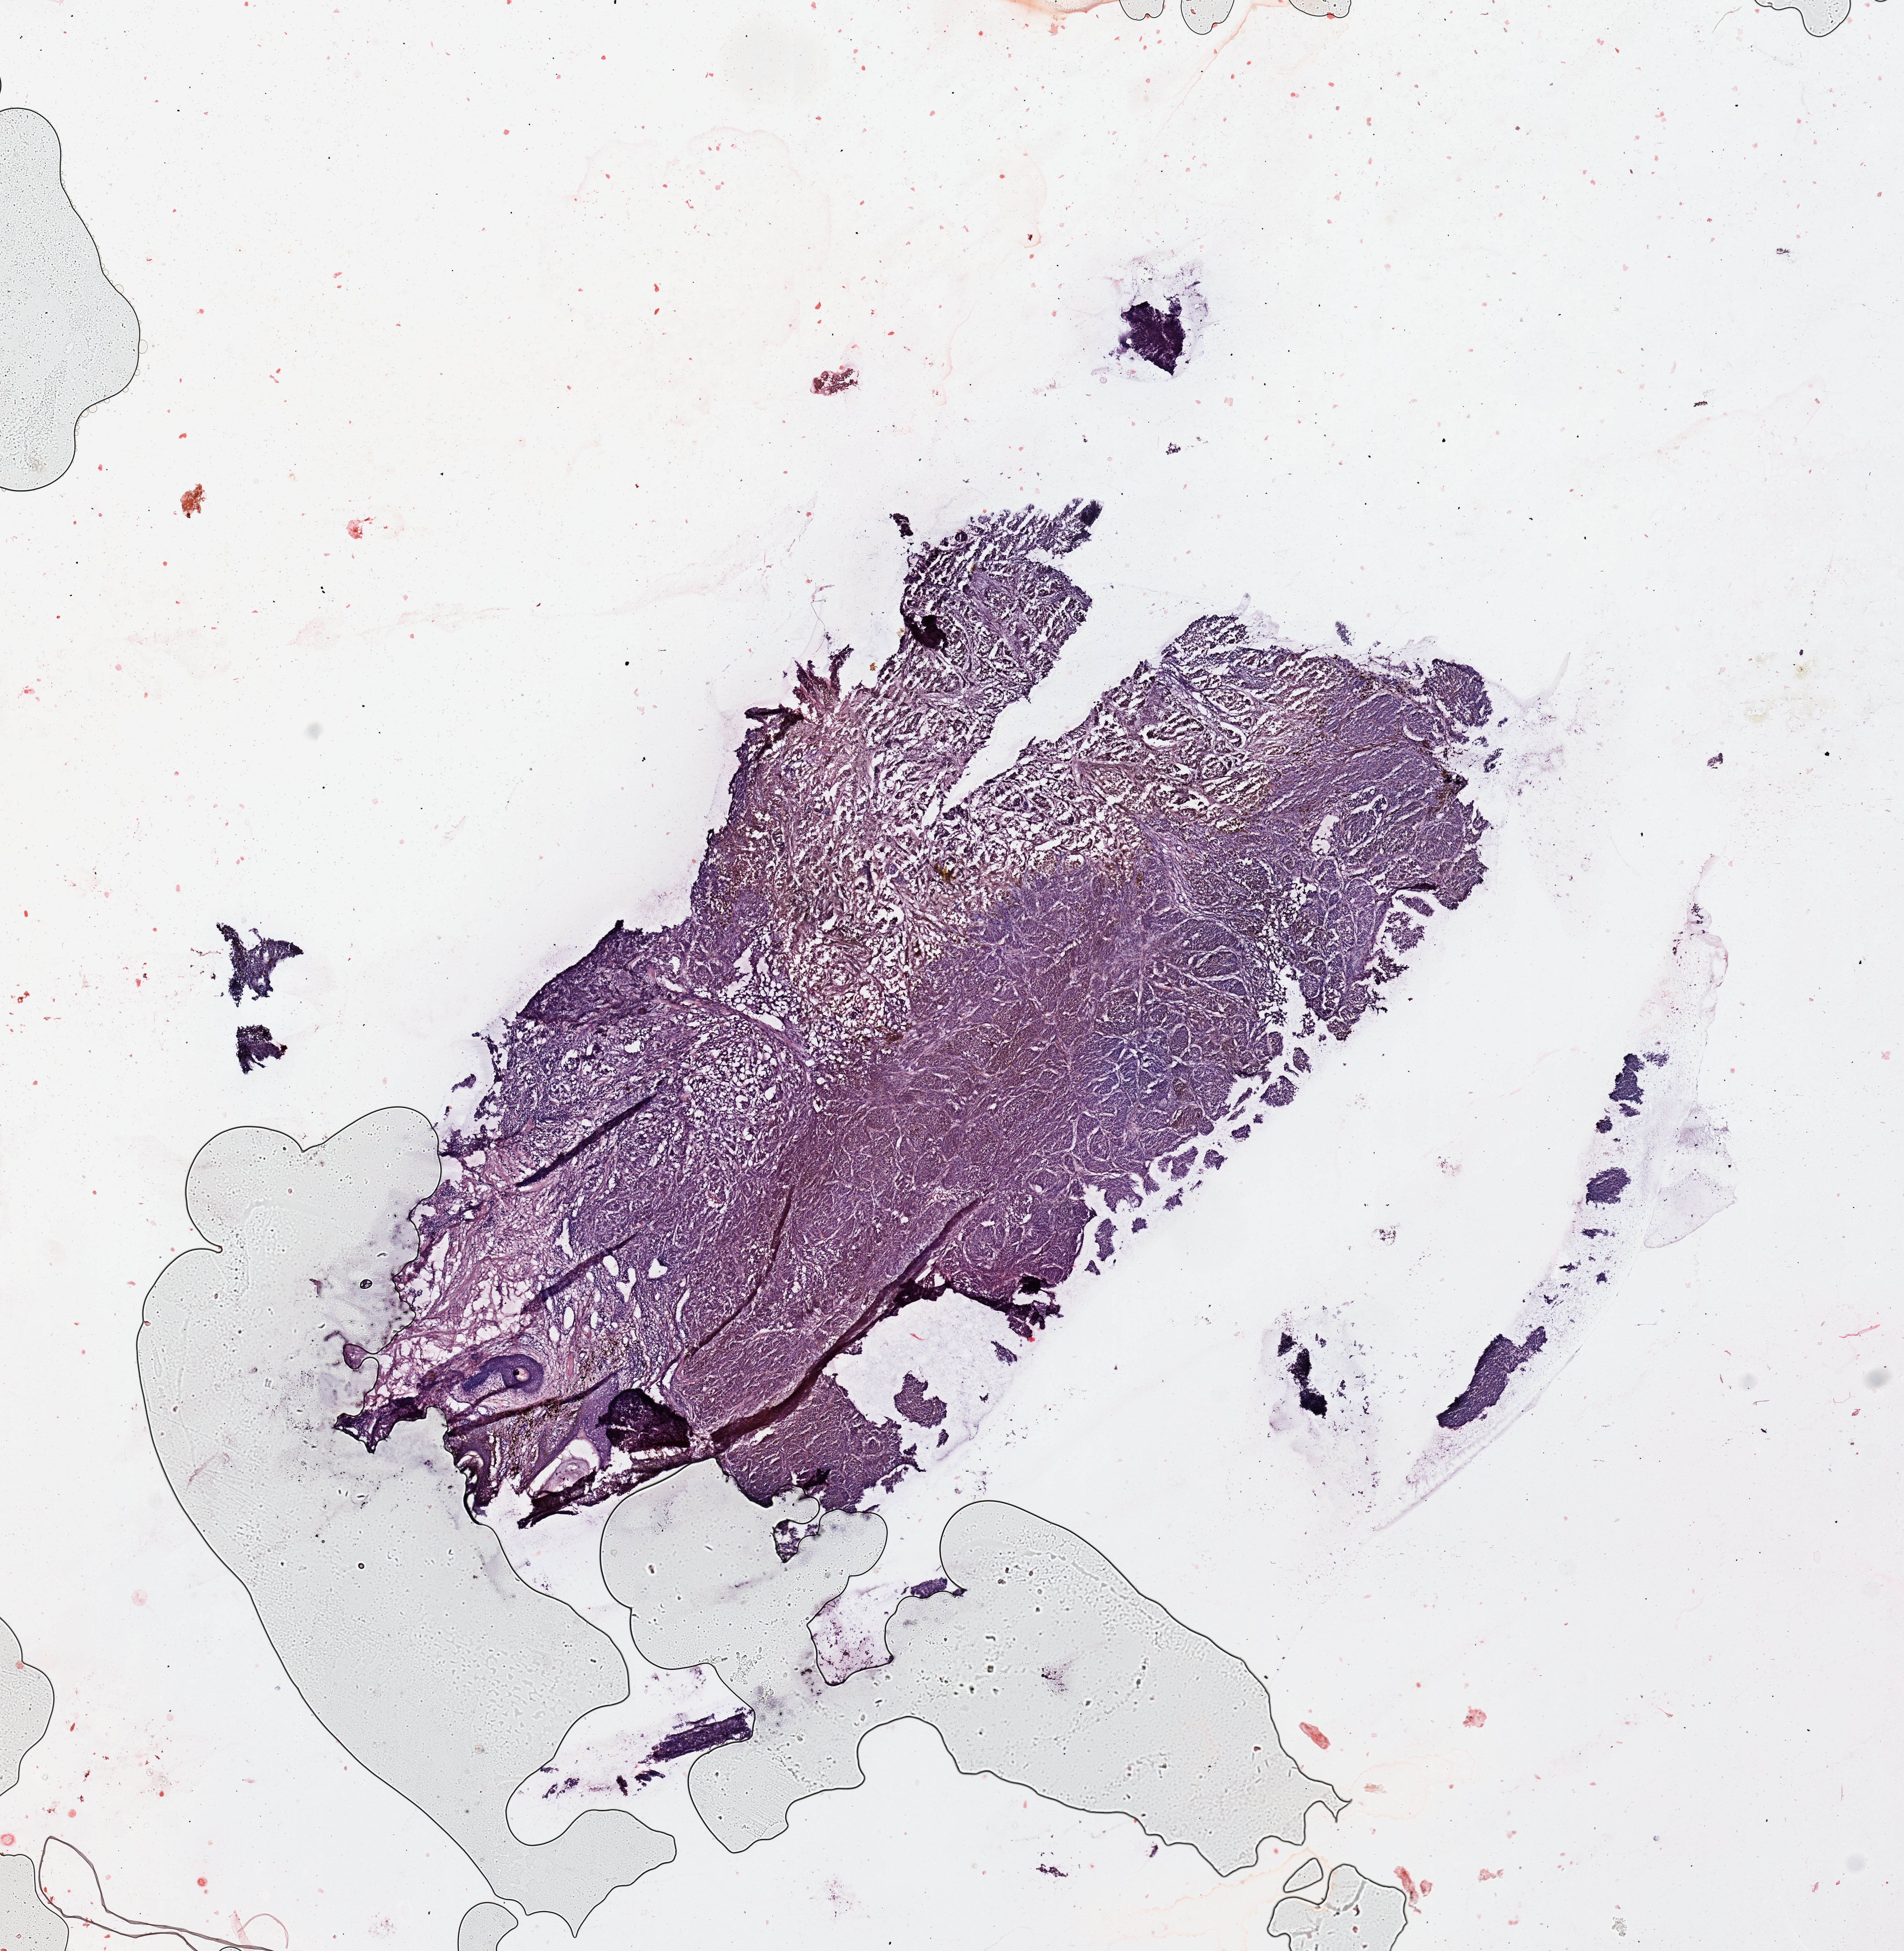
H&E-stained whole-slide image, a low-resolution overview of the entire scanned area, about 11.8 x 12.1 mm (from a 20x scan), melanoma tumour tissue; sampled site not recorded. Male, 54 y/o.
* primary tumour site (as recorded): trunk
* patient diagnosis (cohort enrolment): cutaneous melanoma (skin)